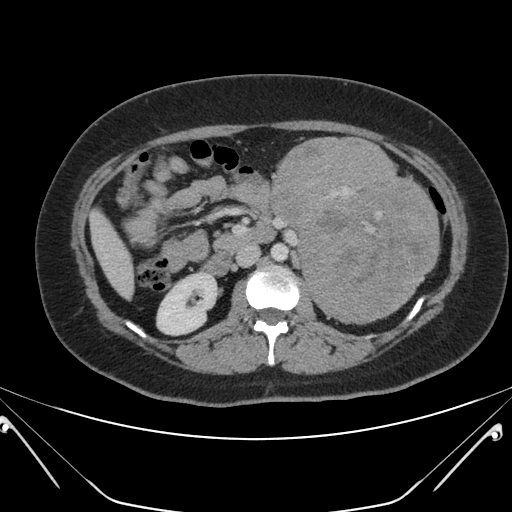
Contrast-enhanced abdominal CT, one axial slice; slice 108 of 168 in the series (ordered by position); 120 kVp; soft-tissue window (W 400 / L 40 HU); 3 mm slice thickness; 512 × 512 image matrix. Female patient, age 26 years. From the clinical record (not read from this slice): diagnosis: adrenocortical carcinoma; tumour side: left adrenal; tumour size at pathology: 28 cm; Ki-67 index: 20 %; stage (as recorded): 2.
Annotated regions visible in this slice (semi-automatic segmentation, software-assisted and operator-edited):
- mass: bounding box (x1, y1, x2, y2) in pixels: (272, 136, 439, 323)